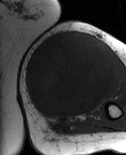
MRI of an extremity soft-tissue mass, one axial slice; slice 33 of 86 in the series (ordered by position); MR volume resampled by the dataset authors to the PET/CT grid (not the native acquisition matrix); 3.27 mm slice thickness; 126 × 155 image matrix. Female patient. From the clinical record (not read from this slice): histological type: pleiomorphic leiomyosarcoma; grade: high; site of the primary tumour: left biceps.
Outlined on this slice (expert contour drawn on MRI and transferred to this co-registered scan by the dataset authors):
- gross tumour volume including surrounding oedema: bounding box (x1, y1, x2, y2) in pixels: (24, 31, 115, 121)
- gross tumour volume (mass): (24, 31, 115, 119)